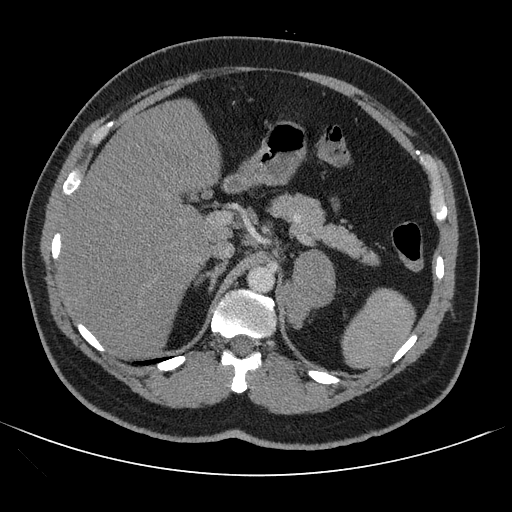
Contrast-enhanced abdominal CT, one axial slice. Position 71 of 121 along the scan axis. Intravenous contrast given. Soft-tissue window (W 400 / L 40 HU). 512 × 512 image matrix, field of view 399 × 399 mm. Male patient, age 53 years. From the clinical record (not read from this slice): diagnosis: adrenocortical carcinoma; tumour side: left adrenal; tumour size at pathology: 7.9 cm; Ki-67 index: 20 %.
Annotated regions visible in this slice (semi-automatic segmentation, software-assisted and operator-edited):
- mass: box from (x=280, y=251) to (x=335, y=326) px